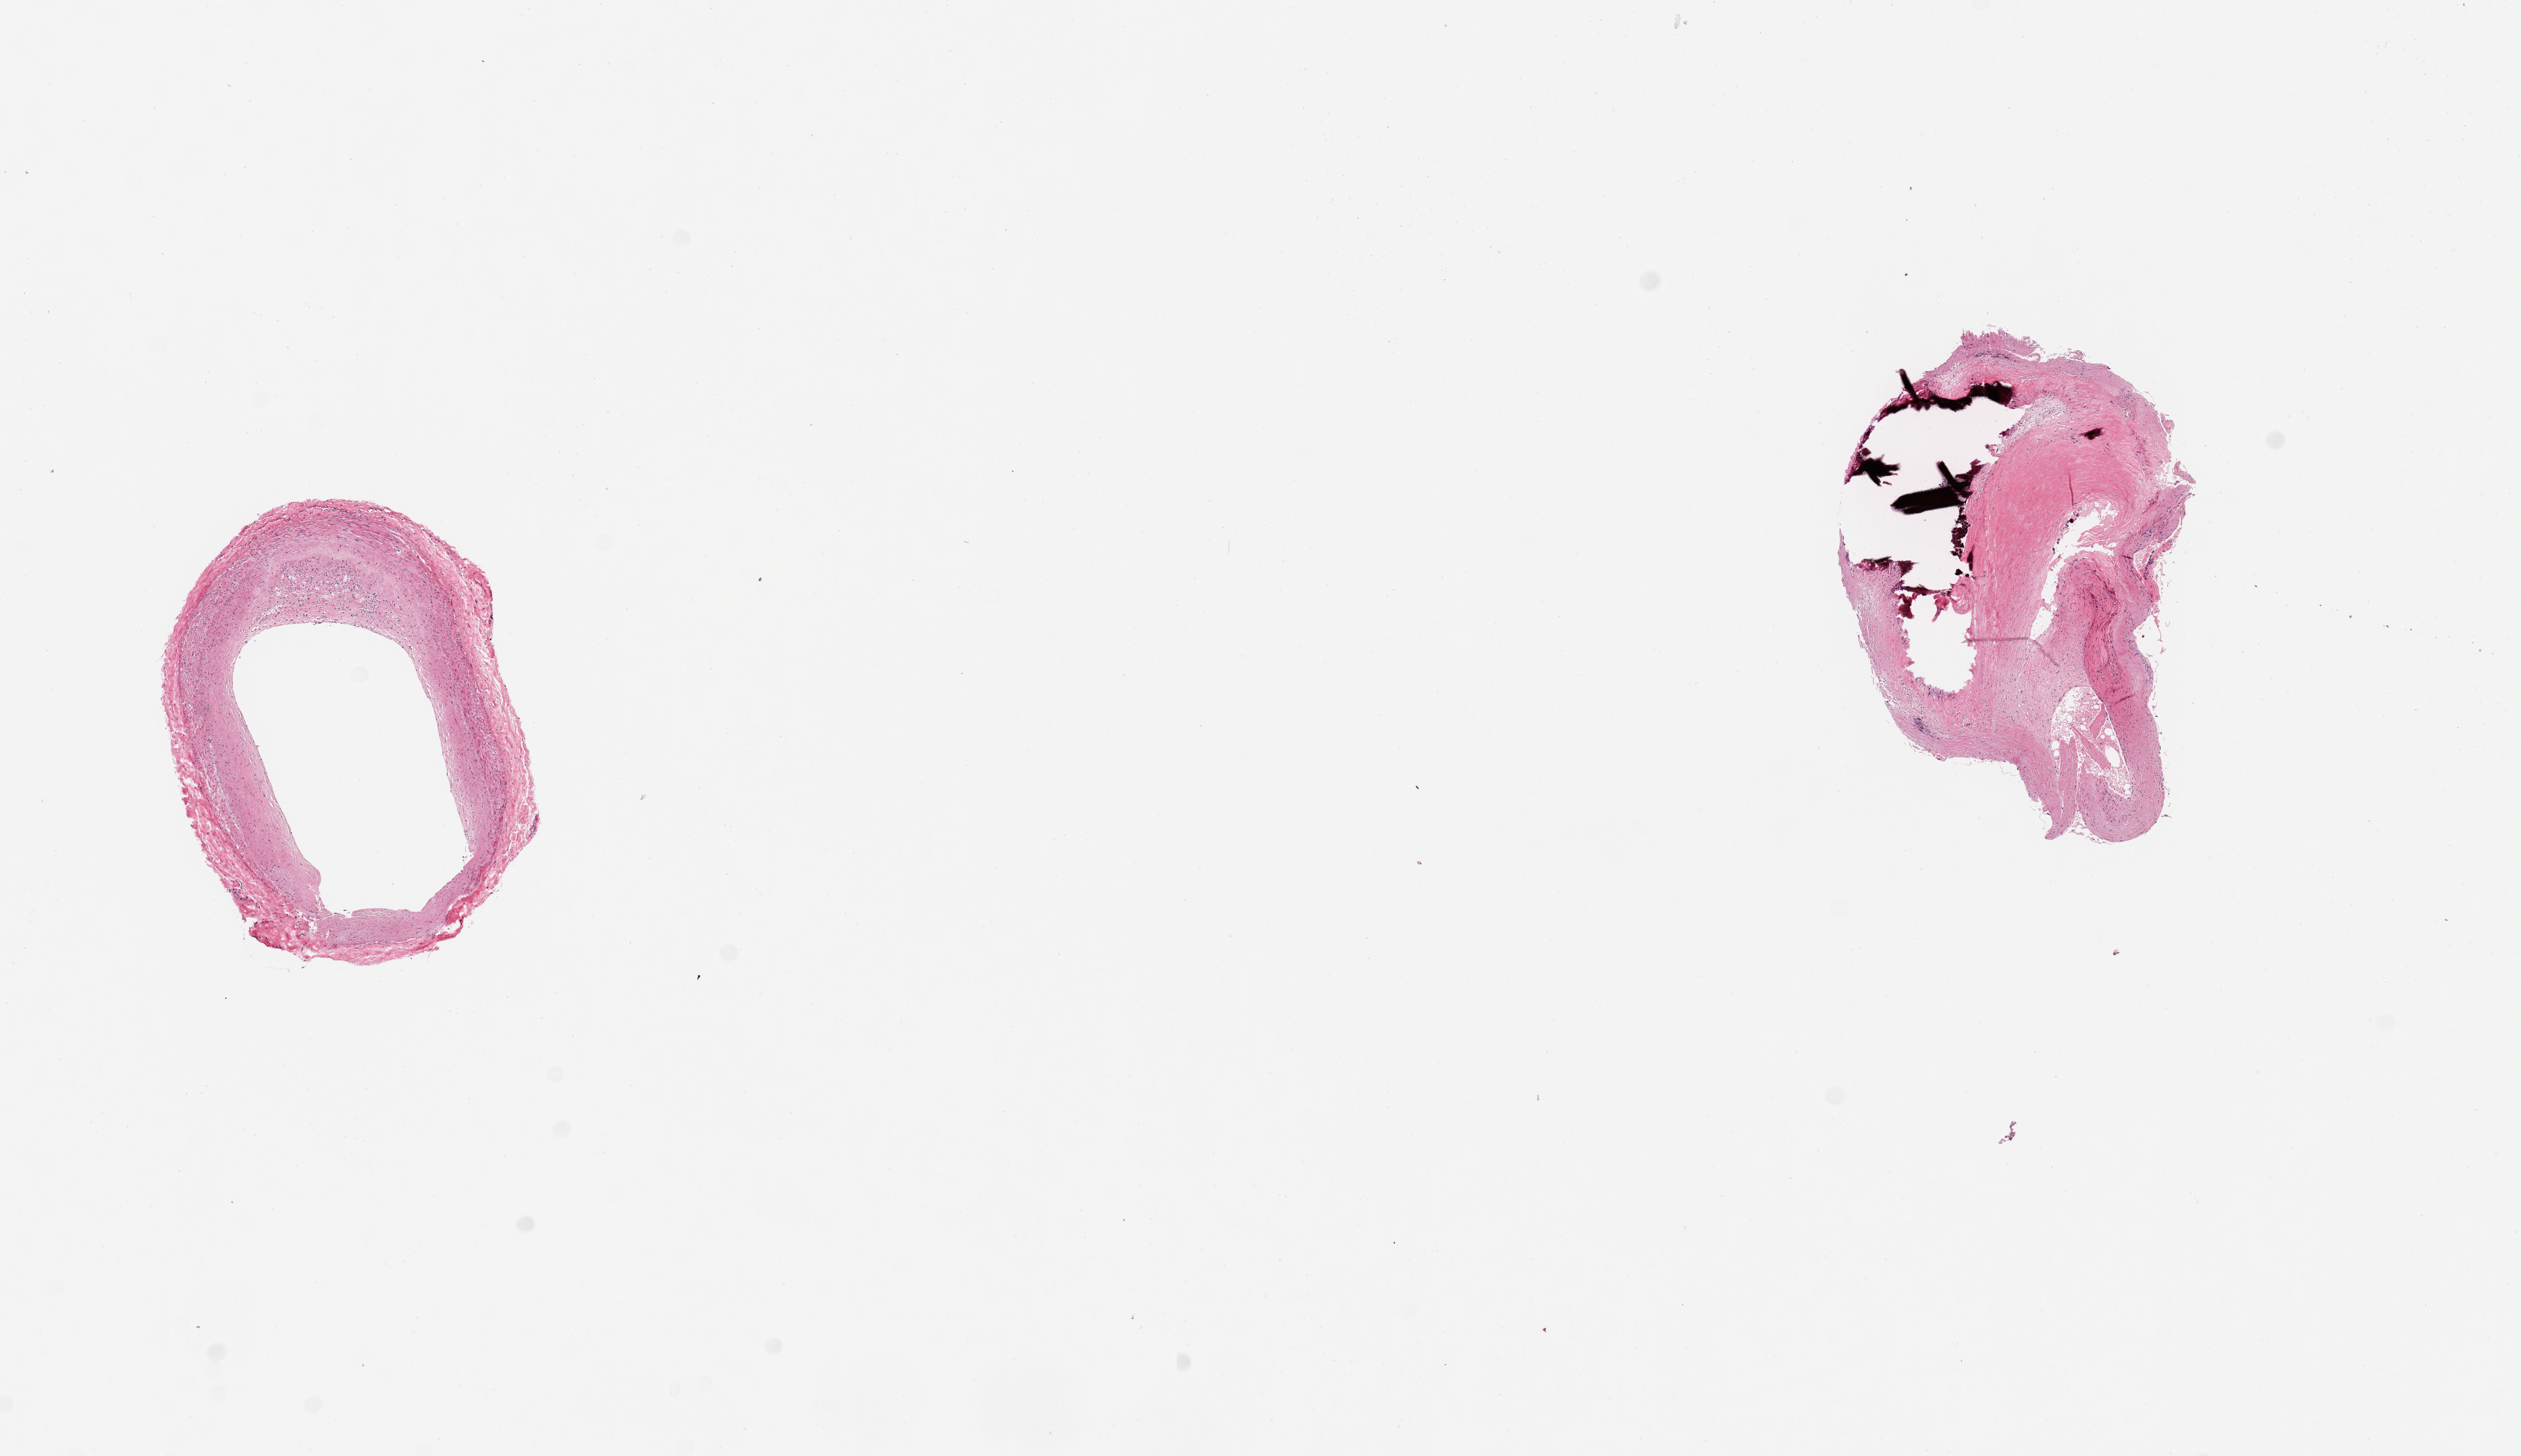
Whole-slide image, hematoxylin and eosin (H&E) stain, a low-resolution overview of the entire scanned area, about 14.8 x 8.5 mm (slide scanned at 20x). PAXgene-fixed paraffin-embedded (PFPE) section. Section of coronary artery (target tissue). Tissue donor sample. Female donor.
Pathologist's review note for this sample: 2 pieces; large calcified atheromatous plaque; well trimmed.